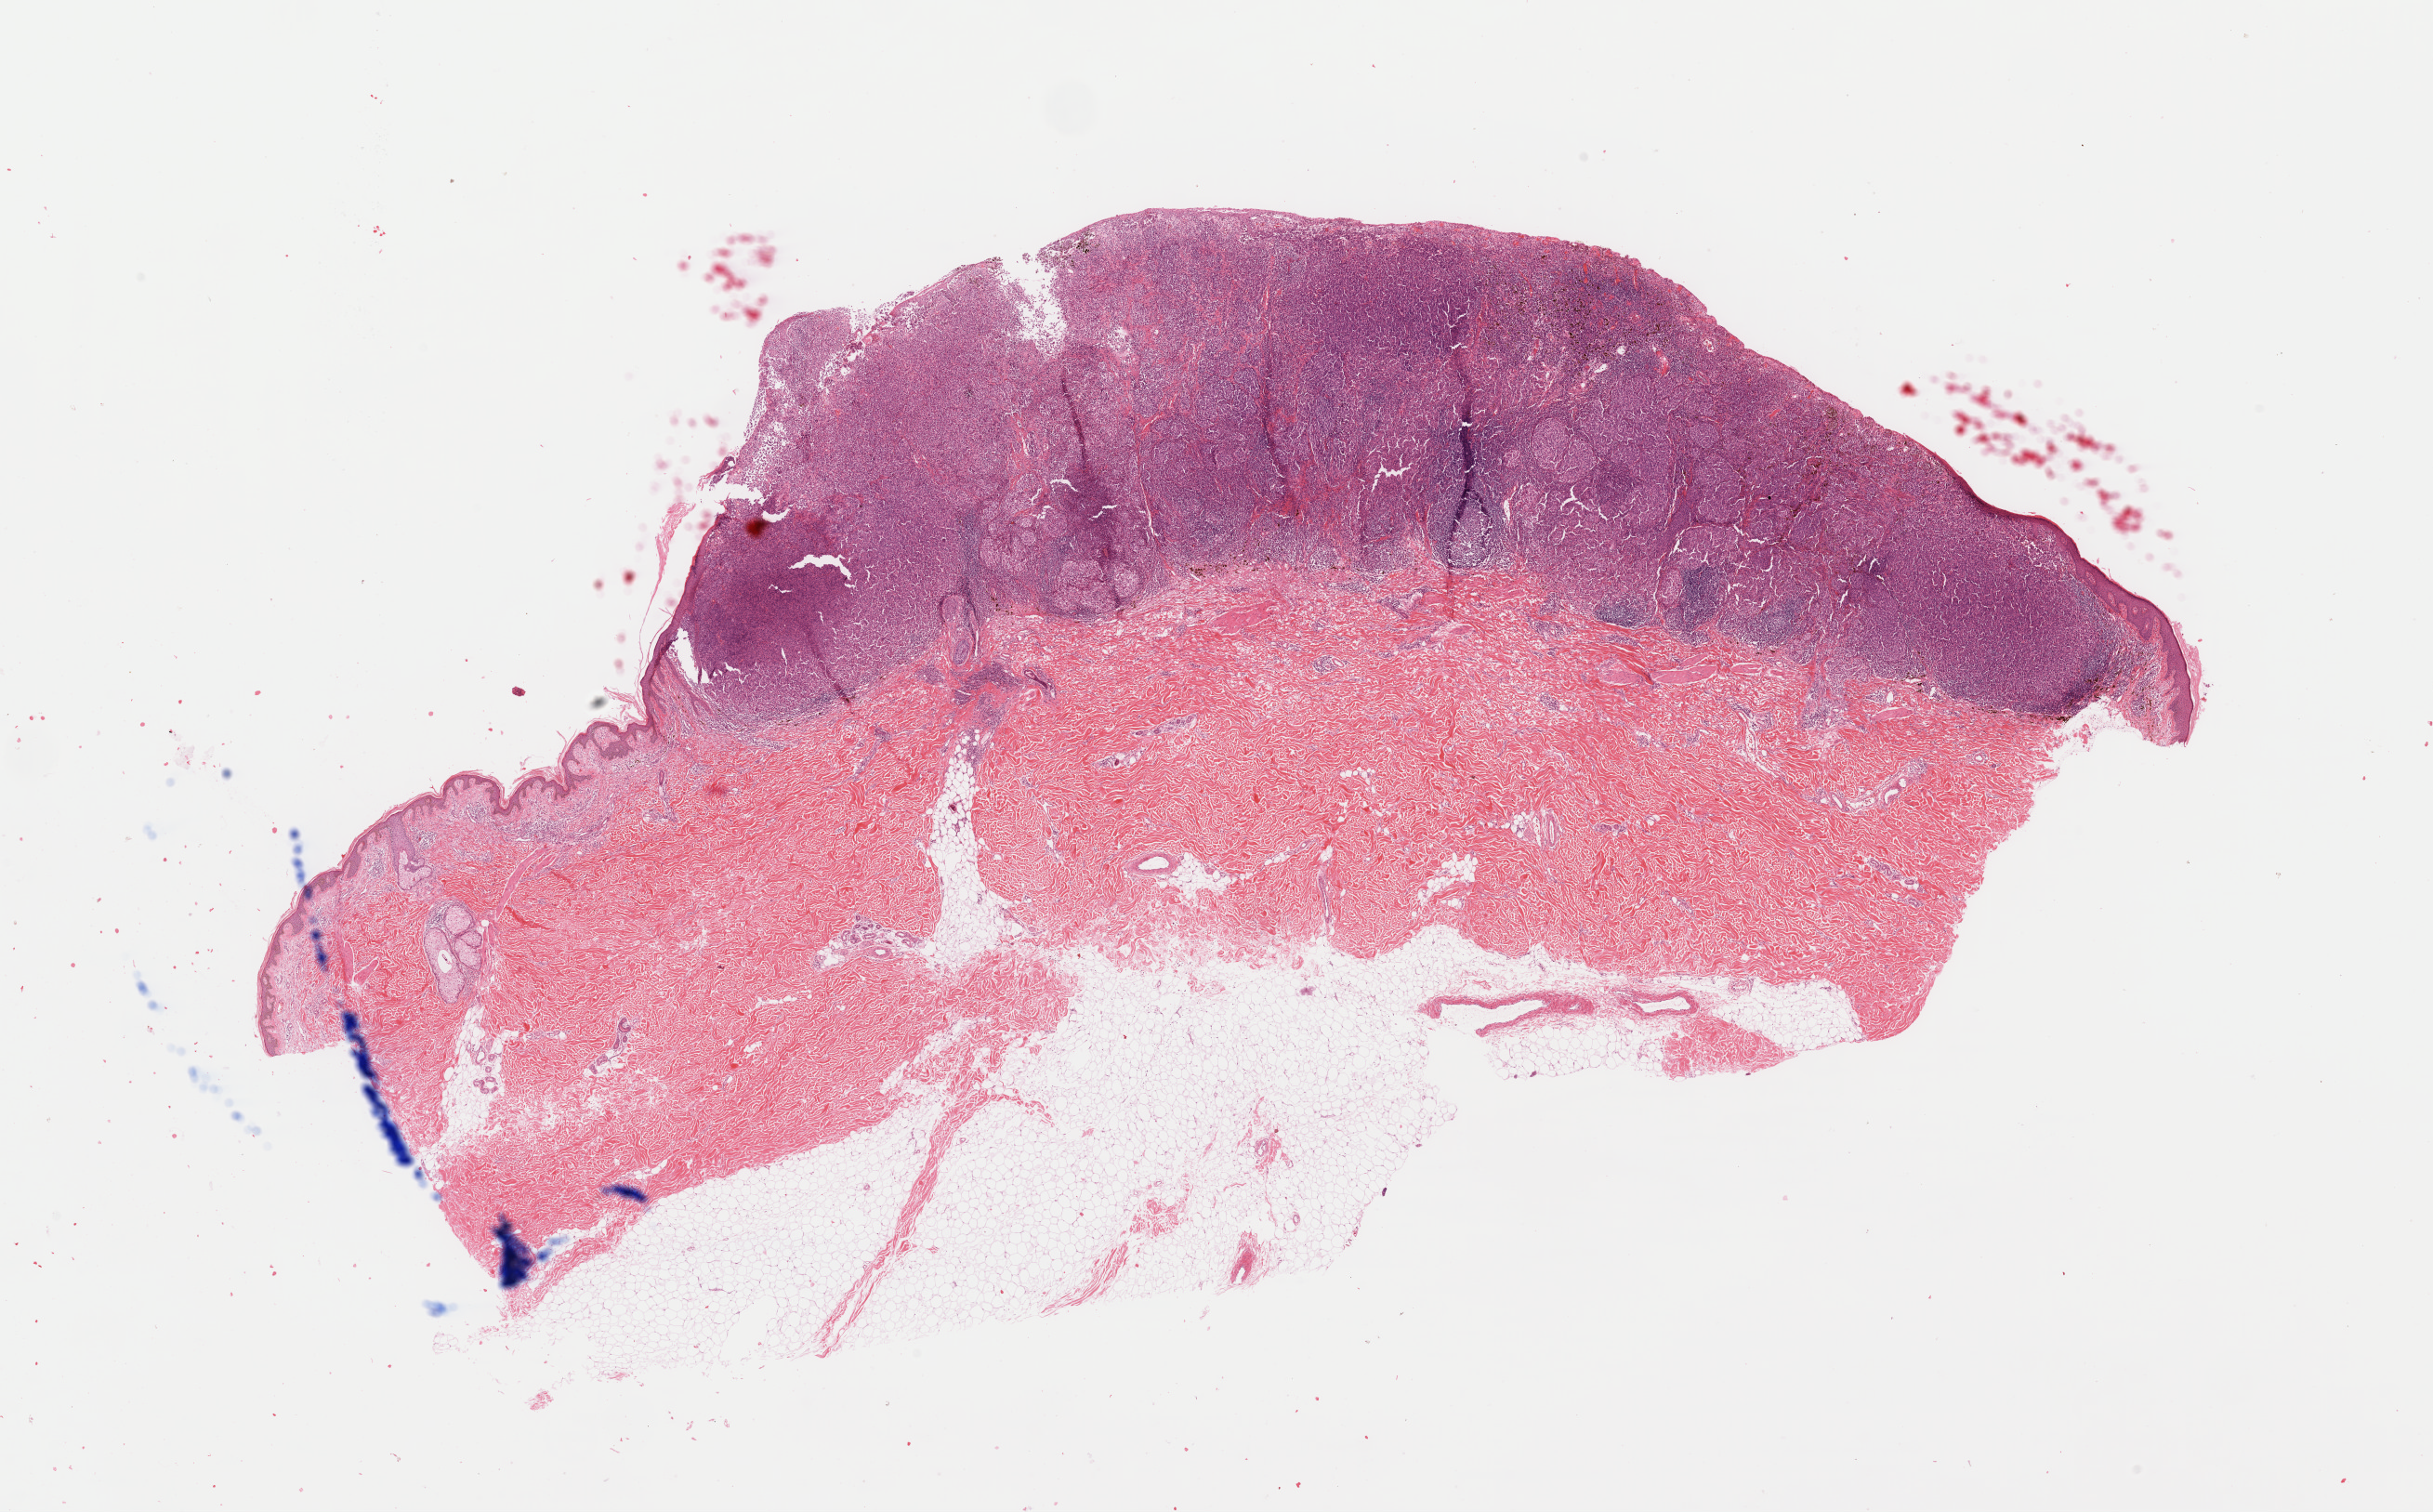
H&E whole-slide image, low-resolution overview of the scanned area, about 20.7 x 12.8 mm (from a 40x scan). Formalin-fixed paraffin-embedded (FFPE) diagnostic section. Primary tumour sample from the skin. Male patient; age at initial diagnosis 77 years.
Histologic diagnosis: Malignant melanoma, NOS. AJCC pathologic stage: IIB (7th edition).